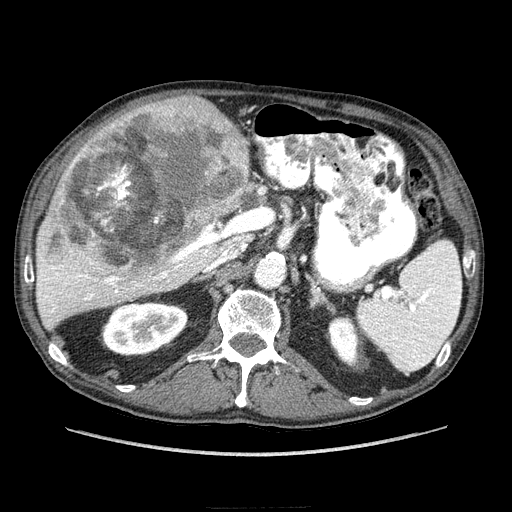
Contrast-enhanced abdominal CT (liver protocol), one axial slice. Slice 141 of 218 in the series (ordered by position). Reconstruction kernel STANDARD. 100 kVp. Soft-tissue window (W 400 / L 40 HU). 2.5 mm slice thickness. 512 × 512 image matrix, field of view 380 × 380 mm. From the clinical record (not read from this slice): diagnosis: hepatocellular carcinoma (patient treated with transarterial chemoembolisation; whether this scan precedes or follows treatment is not stated here); TNM stage (as recorded): Stage-IIIA; Child-Pugh class: A; tumour nodularity: multinodular; tumour size: 20 cm.
Structures marked on this image (semi-automatic segmentation, software-assisted and operator-edited):
- liver parenchyma outside the tumour (the mass and vessels are separate outlines, so this box may not span the whole liver): bounding box [x1, y1, x2, y2] px = [36, 104, 266, 328]
- mass: [37, 96, 247, 279]
- liver vessels: [38, 187, 265, 312]